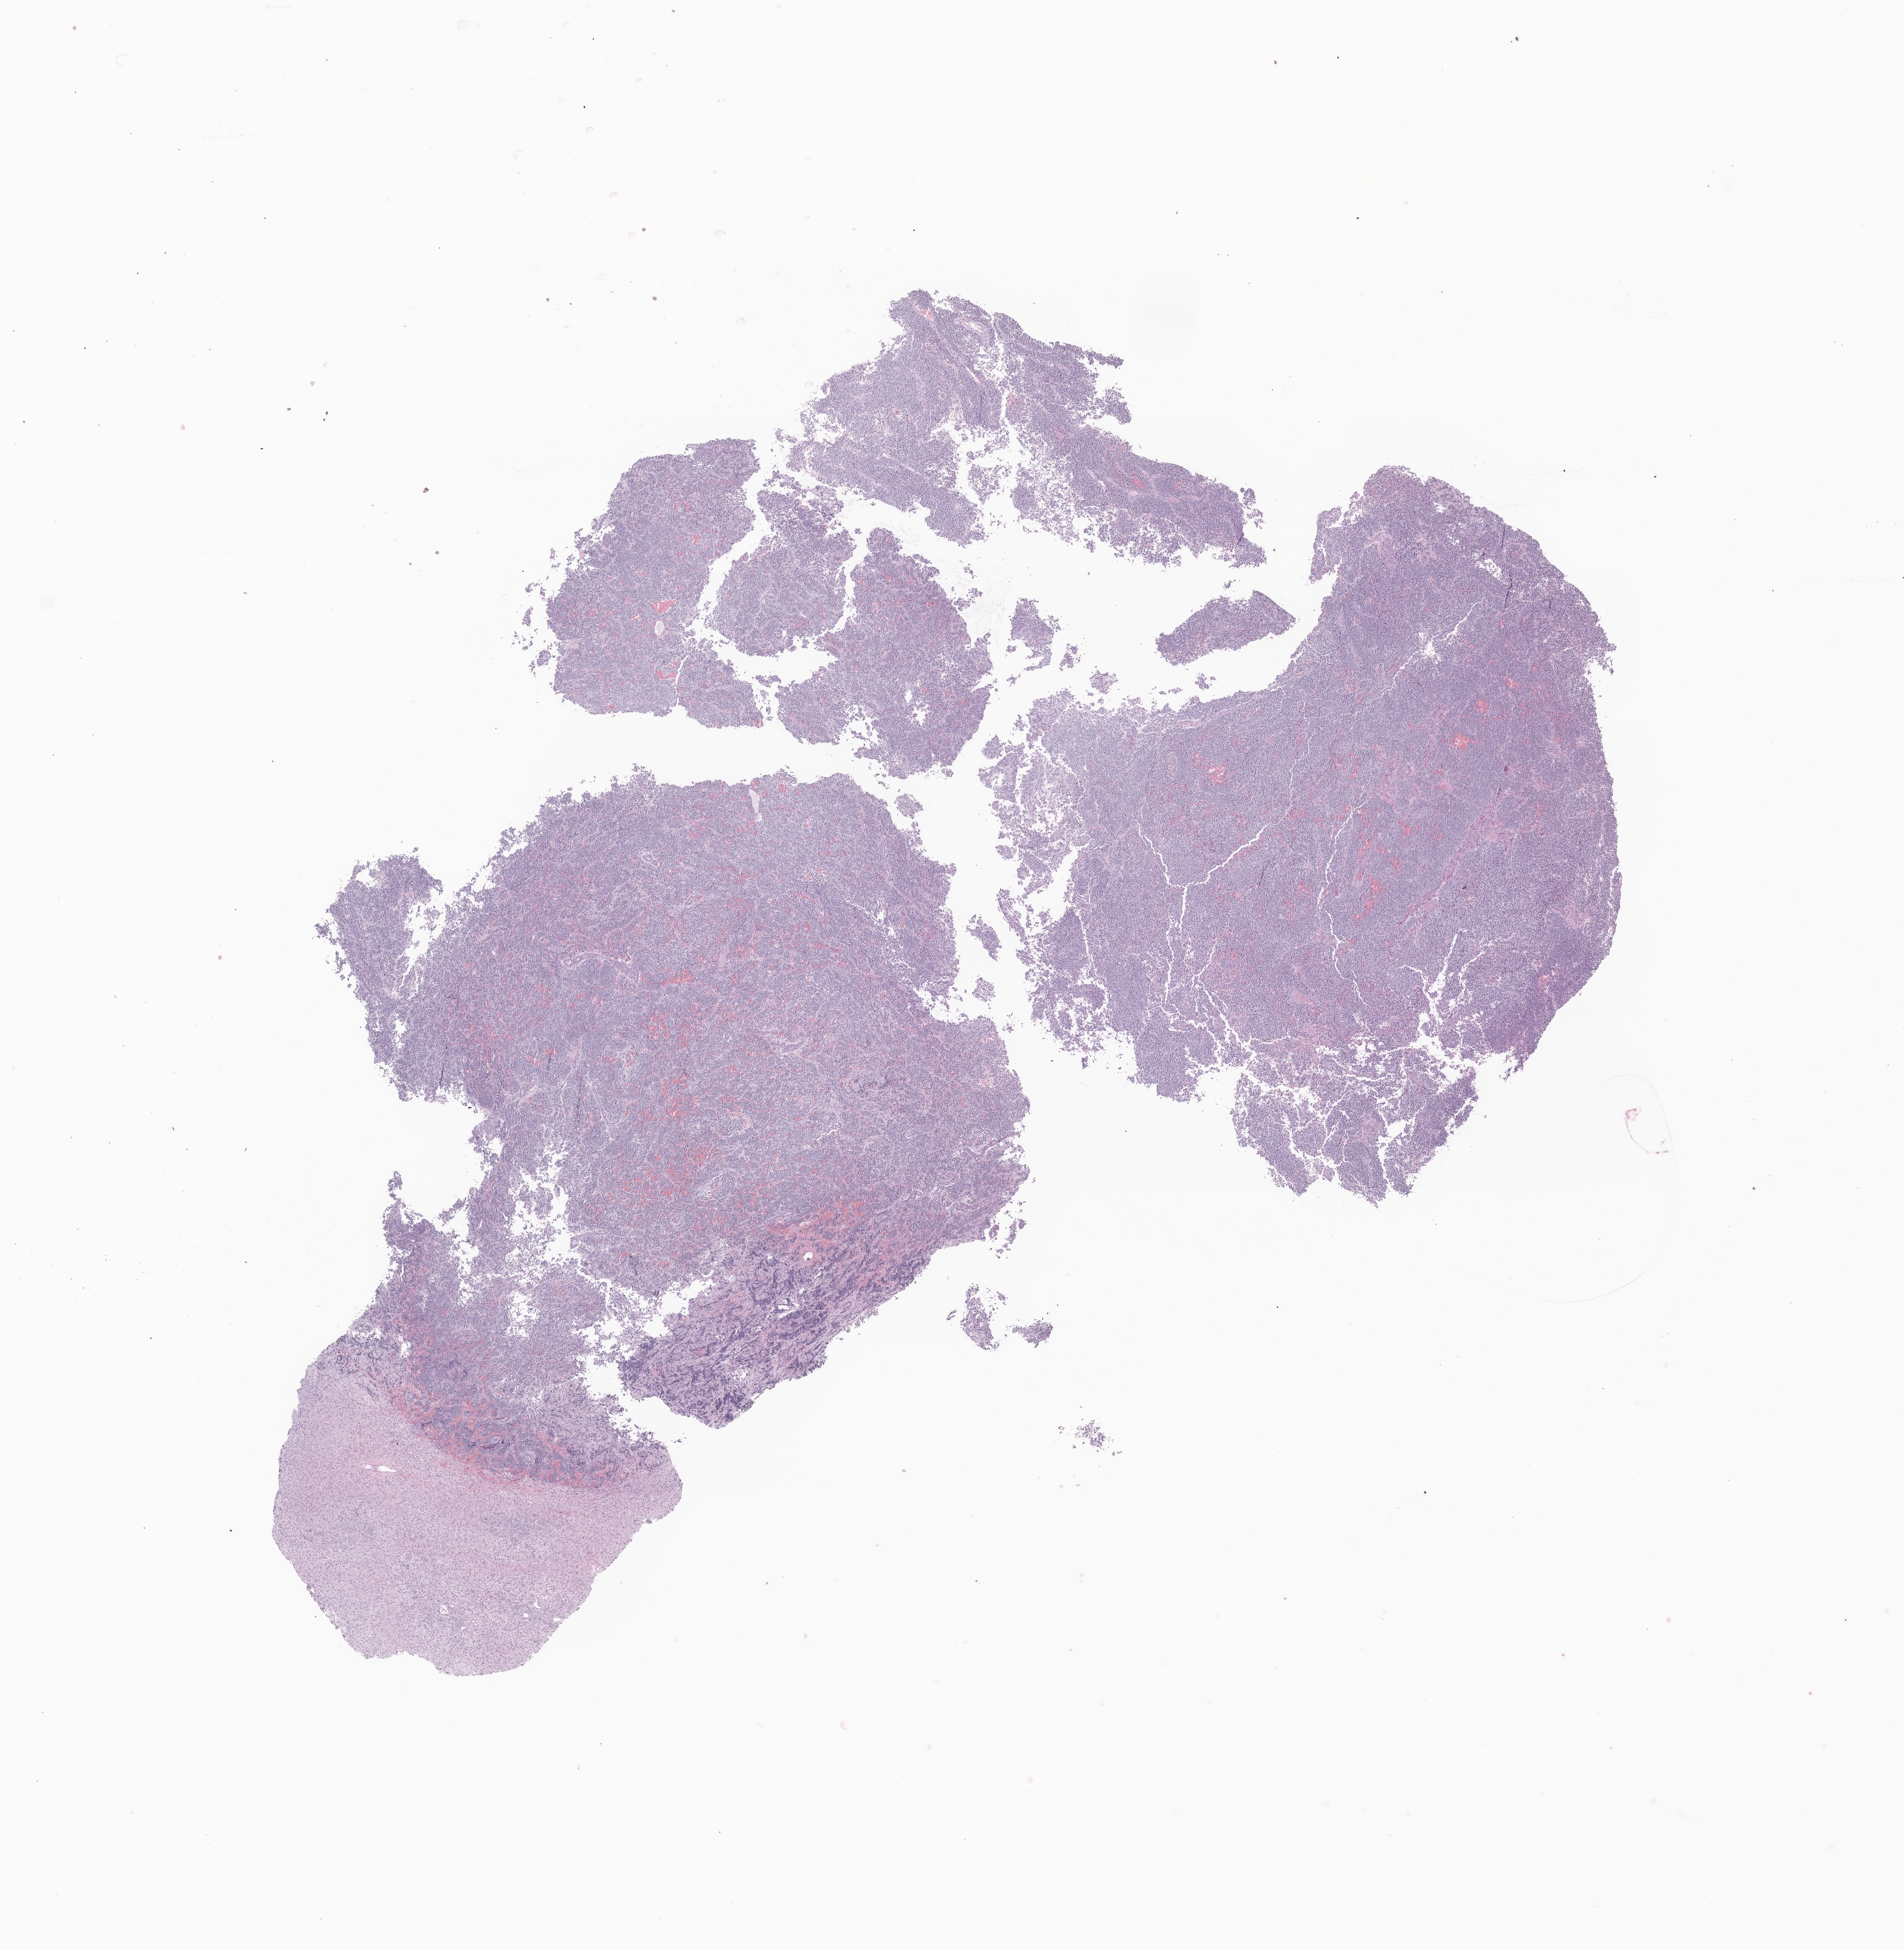
Whole-slide image, haematoxylin and eosin stain of tumor tissue from the abdomen — a low-resolution overview of the entire scanned area, about 13.2 x 13.5 mm, formalin-fixed paraffin-embedded section. Patient female; age 747 days (about 2.0 years).
Recorded diagnosis: Neuroblastoma, NOS.